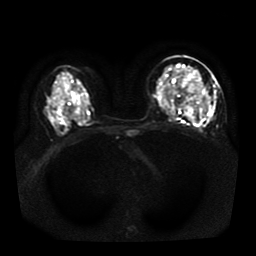
Breast MRI, one axial slice. Position 24 of 41 along the scan axis. Diffusion-weighted series; image 2 of 4 stored at this slice position (different b-values; order by instance number). 1.5 T. 5 mm slice thickness. 256 × 256 image matrix, field of view 330 × 330 mm. Female patient.
Outlined on this slice (outlined manually by an expert reader):
- tumour on diffusion-weighted imaging: bounding box <186,84,210,115> (left, top, right, bottom; pixels)